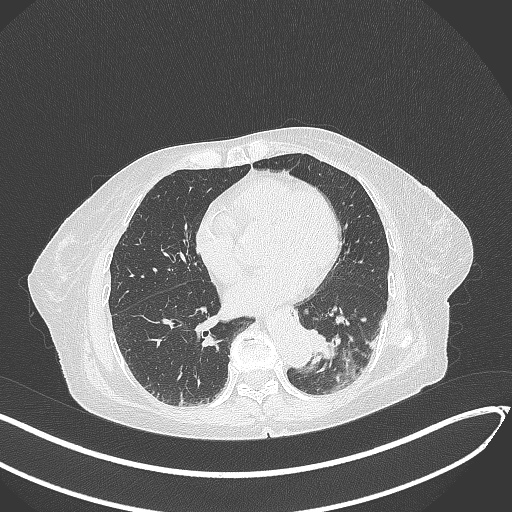
Chest CT, one axial slice; position 91 of 324 along the scan axis; reconstruction kernel B70f; 120 kVp; lung window (W 1500 / L -600 HU); 512 × 512 image matrix. Patient: female, 82 years. Case-level facts recorded for this patient, not image findings: clinical TNM (as recorded): T1b N0 M1.
Structures marked on this image (rectangle marked by the reading radiologist):
- lung tumour (recorded histology: adenocarcinoma): bounding box <306,325,351,368> (left, top, right, bottom; pixels)